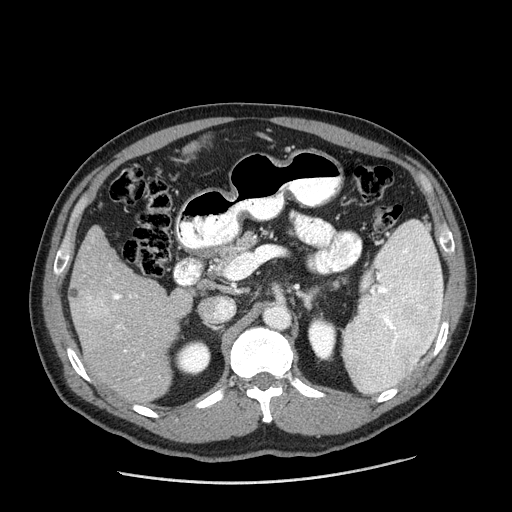
Contrast-enhanced abdominal CT (liver protocol), one axial slice; slice 91 of 198 in the series (ordered by position); reconstruction kernel STANDARD; one of 2 acquisitions stored at this slice position; soft-tissue window (W 400 / L 40 HU); 2.5 mm slice thickness; 512 × 512 image matrix, field of view 400 × 400 mm. From the clinical record (not read from this slice): diagnosis: hepatocellular carcinoma (patient treated with transarterial chemoembolisation; whether this scan precedes or follows treatment is not stated here); TNM stage (as recorded): Stage-II; Child-Pugh class: A; tumour differentiation: moderately differentiated; tumour nodularity: multinodular.
Structures marked on this image (semi-automatically segmented with operator editing):
- liver parenchyma outside the tumour (the mass and vessels are separate outlines, so this box may not span the whole liver): box from (x=70, y=226) to (x=192, y=400) px
- mass: (x=68, y=285)–(x=109, y=318)
- liver vessels: (x=113, y=293)–(x=141, y=380)